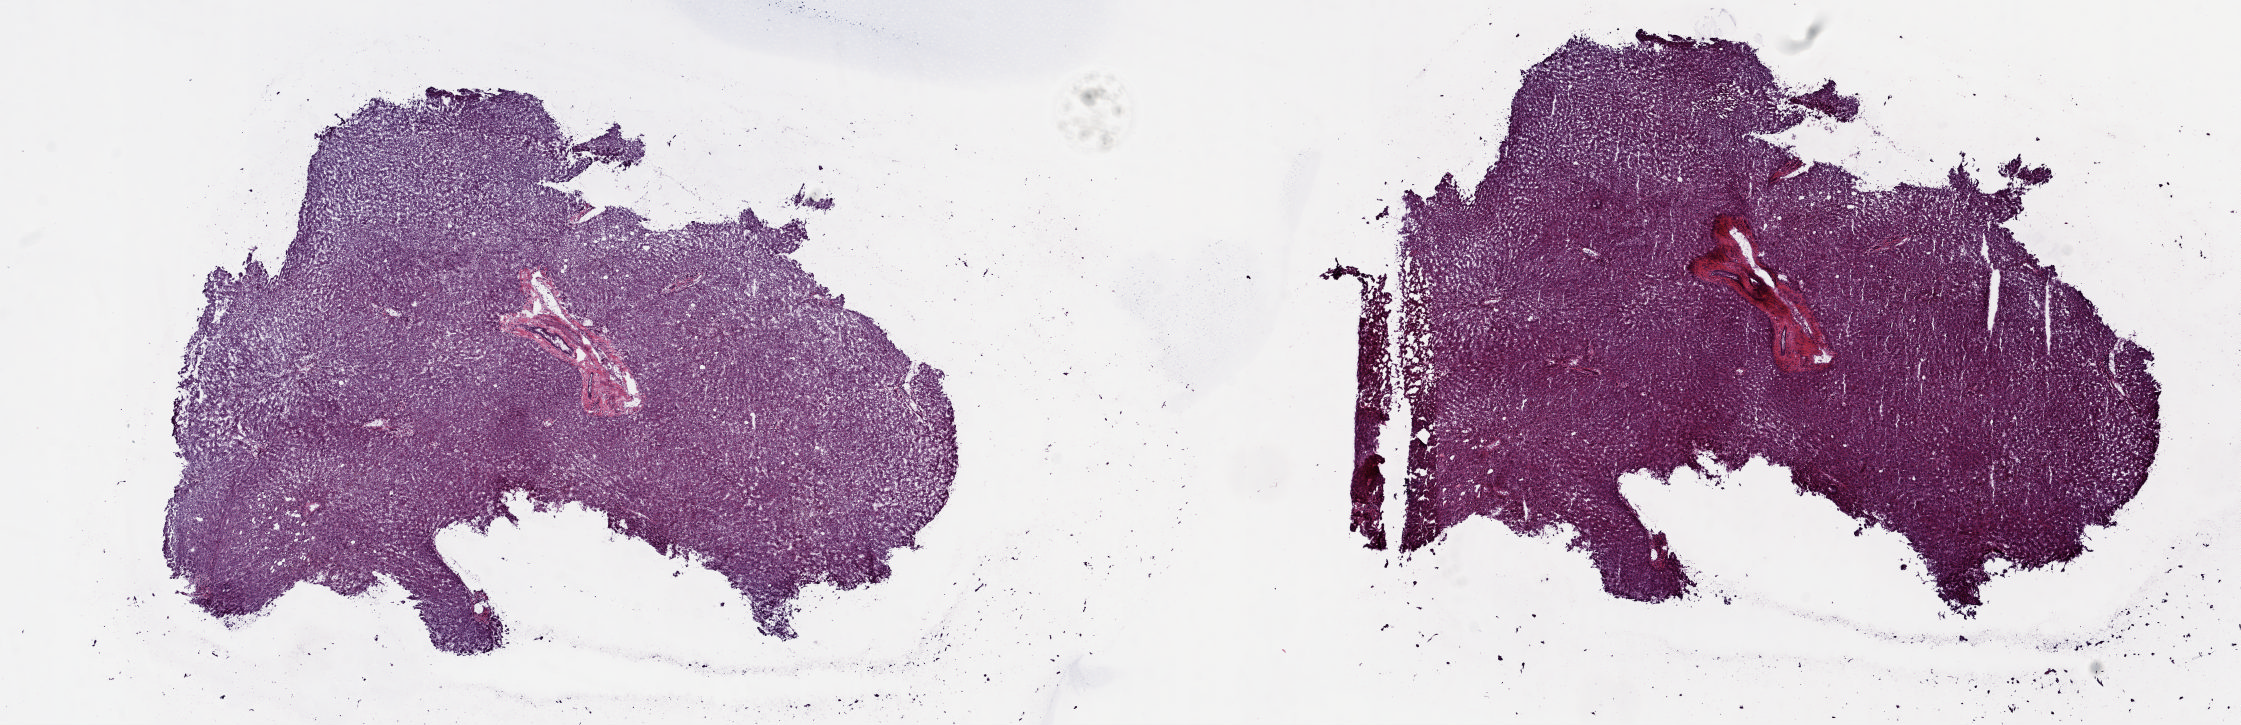
Digitized Hematoxylin and eosin (H&E) stained tissue section (whole slide), a low-resolution overview of the entire scanned area, about 17.8 x 5.8 mm (acquisition: 20x scan). Frozen section from the top of the tissue portion. Liver, solid tissue normal (non-tumour tissue) sample. Male, age 53 years at initial diagnosis.
This section: solid tissue normal sample (biorepository sample class). Patient diagnosis: Hepatocellular carcinoma, NOS.